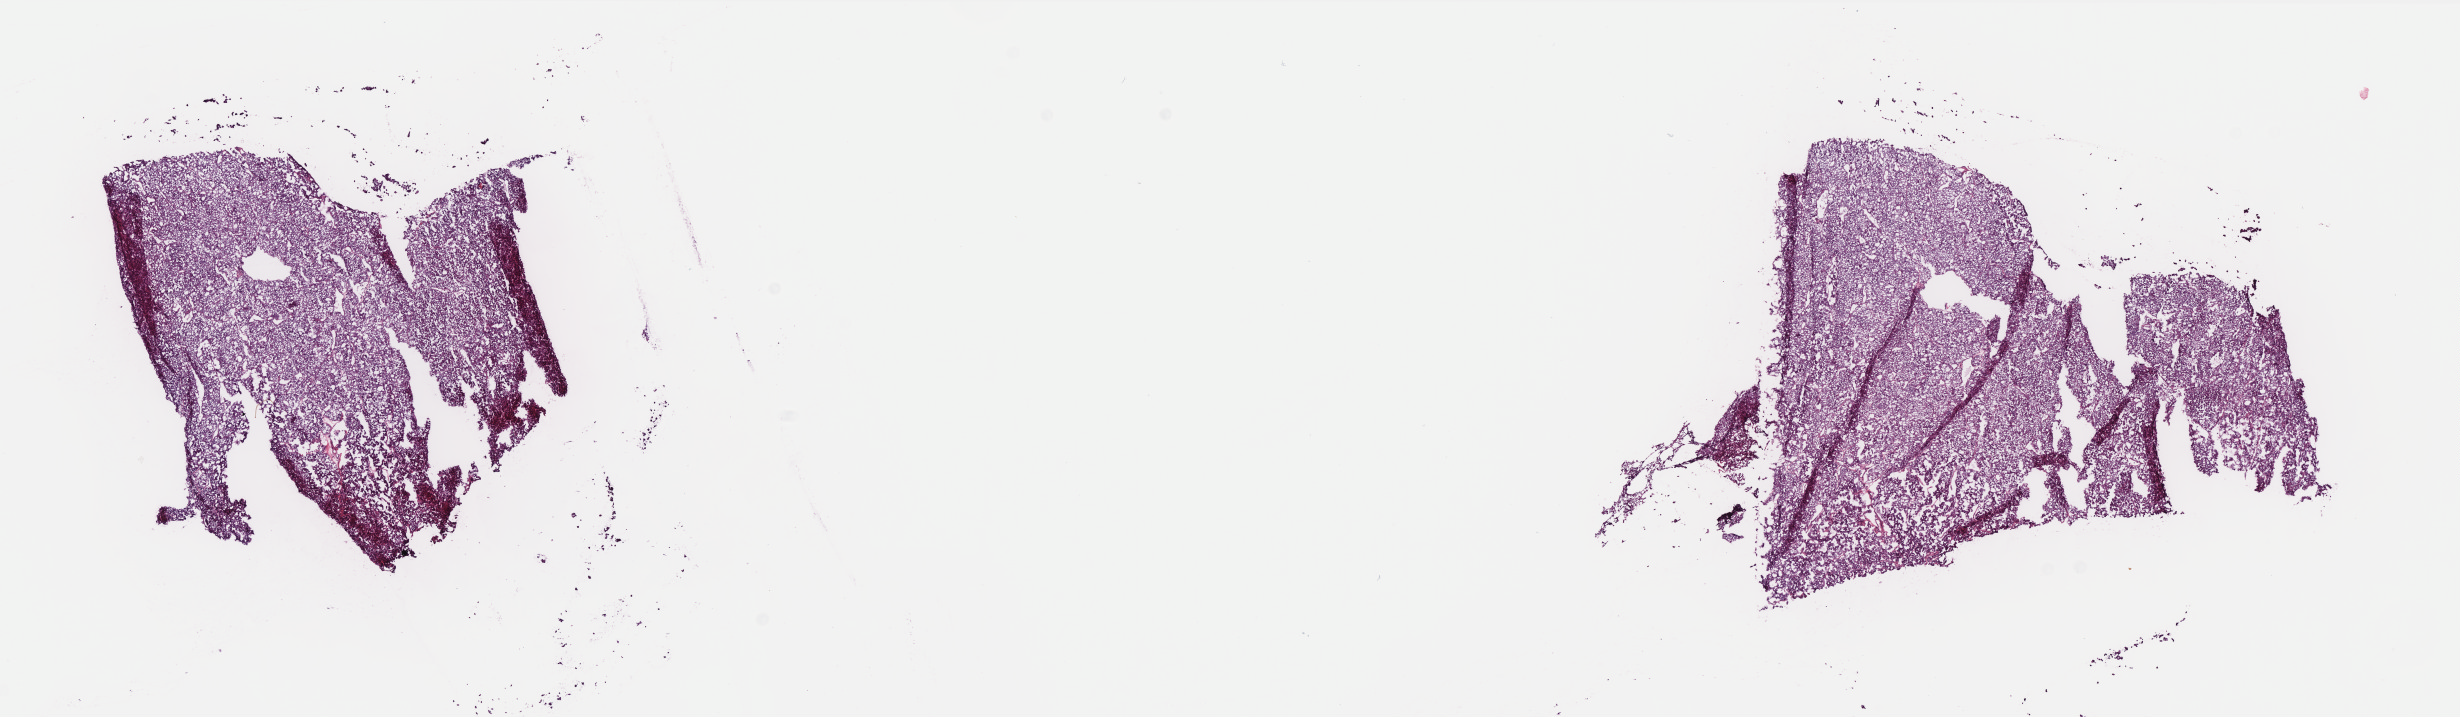
H&E-stained whole-slide image, shown as a low-resolution overview of the whole scanned area (about 19.7 x 5.7 mm, slide scanned at 40x); frozen section from the top of the tissue portion; primary tumour sample from the kidney. Male, age 38 years at initial diagnosis. Pathologist review of this section (percent, as recorded): tumour cells 90%, tumour nuclei 95%, normal cells 0%, stromal cells 0%, necrosis 10%. Inflammatory infiltration, as recorded: lymphocyte infiltration 0%, monocyte infiltration 0%, neutrophil infiltration 0%.
Pathologic diagnosis: Renal cell carcinoma, chromophobe type. AJCC pathologic stage: I (7th edition). TNM: T1b NX.